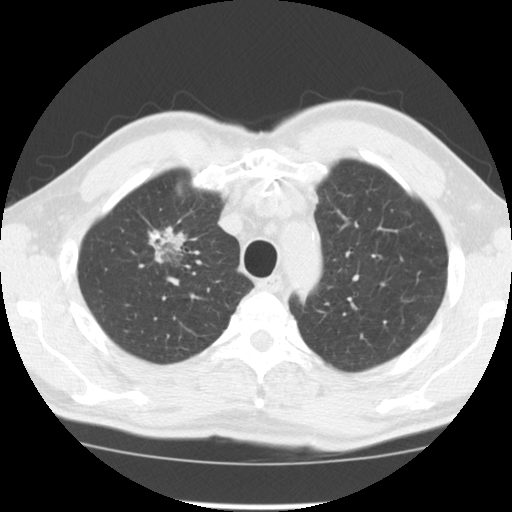
Axial slice from a low-dose chest CT screening exam, third annual screen, lung window (W 1500 / L -600 HU), 2.5 mm slice thickness, standard (soft-tissue) reconstruction kernel (STANDARD), slice 29 of 128 in the series. Male, age 64 years at enrolment.
Expert reader's lesion annotation, bounding box [x1, y1, x2, y2] px = [128, 219, 206, 283]. The screening reader recorded 3 non-calcified nodules or masses ≥4 mm on this exam (right upper lobe, right lower lobe, left upper lobe); which of them this box marks is not recorded. Official screen result: positive, other. Later outcome: lung cancer diagnosed 30 days after this screen — adenocarcinoma, NOS, right upper lobe, well differentiated (G1), stage IB (AJCC 6th edition), 45 mm at pathology.